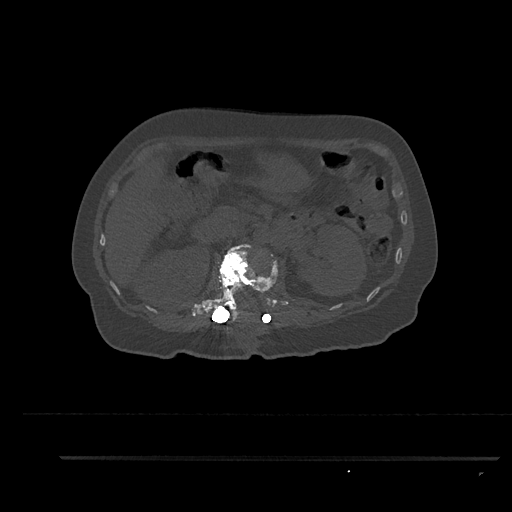
CT including the spine, one axial slice; position 206 of 797 along the scan axis; 120 kVp; bone window (W 1800 / L 400 HU); 0.5 mm slice thickness; 512 × 512 image matrix, field of view 408 × 408 mm. Female patient, age 44 years. From the clinical record (not read from this slice): primary cancer: renal; vertebrae with lytic lesions (as recorded): L1.
Annotated regions visible in this slice (semi-automatically segmented with operator editing):
- L1 vertebra: box from (x=203, y=244) to (x=278, y=322) px